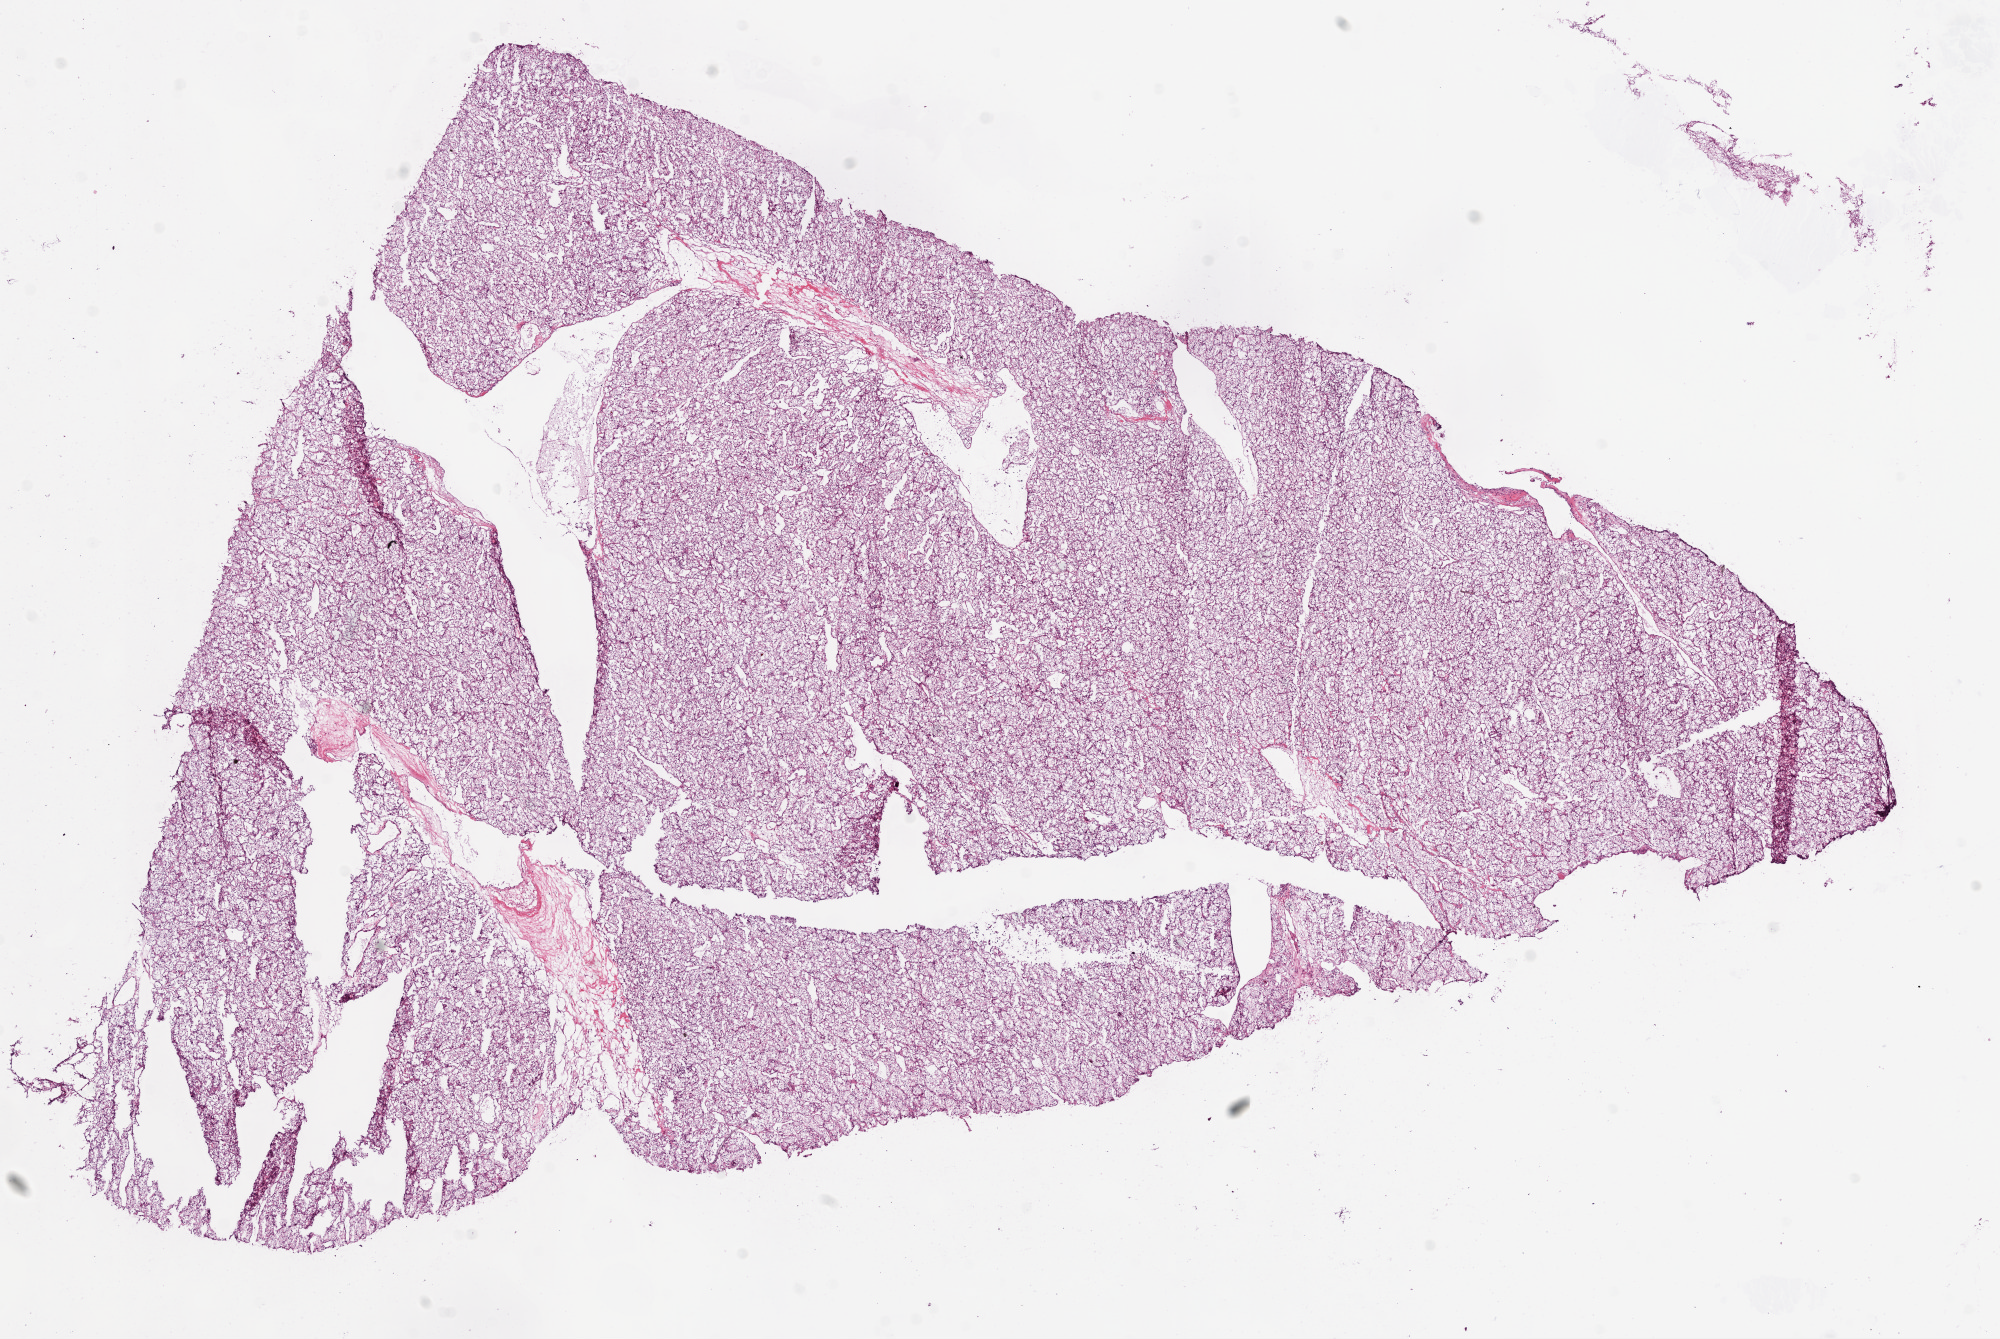
H&E whole-slide image — shown as a low-resolution overview of the whole scanned area (about 16.0 x 10.7 mm). Frozen section from the bottom of the tissue portion. Kidney, primary tumour sample. Male, age 69 years at initial diagnosis. Histologic grade: G2 (moderately differentiated). Slide review estimates, as recorded: tumour cells 95%, tumour nuclei 90%, normal cells 0%, stromal cells 5%, necrosis 0%.
Laterality: right. AJCC pathologic stage: I. Pathologic diagnosis: Clear cell adenocarcinoma, NOS. Lymph nodes positive (case pathology): 0 of 5 examined.